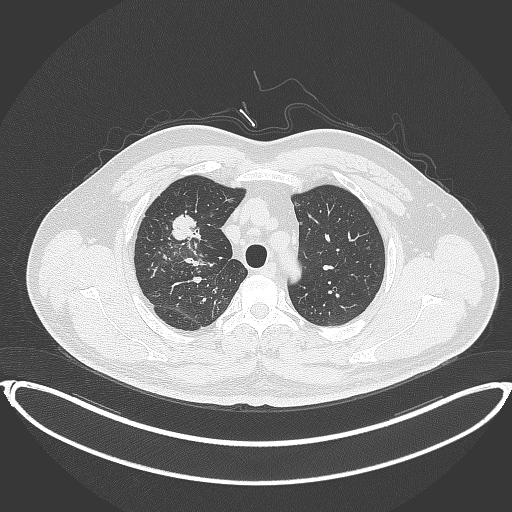
Chest CT, one axial slice. Slice 304 of 399 in the series (ordered by position). Reconstruction kernel B70f. Lung window (W 1500 / L -600 HU). 1 mm slice thickness. 512 × 512 image matrix. Male patient, age 53 years. From the clinical record (not read from this slice): clinical TNM (as recorded): T2a N0 M0.
Structures marked on this image (rectangle marked by the reading radiologist):
- lung tumour (recorded histology: adenocarcinoma): box from (x=168, y=211) to (x=203, y=244) px